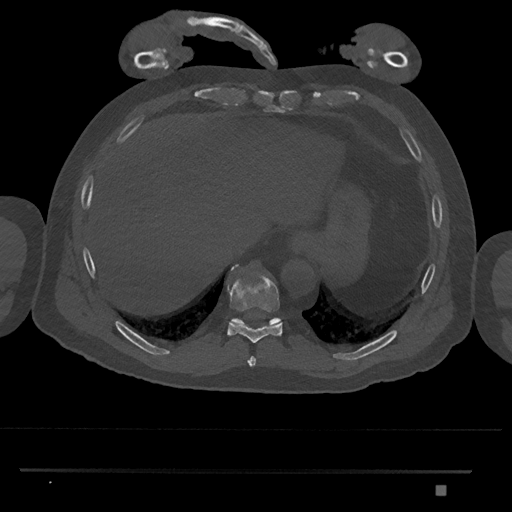
CT including the spine, one axial slice; position 1045 of 1134 along the scan axis; reconstruction kernel Br40s/3; bone window (W 1800 / L 400 HU); 0.5 mm slice thickness; 512 × 512 image matrix, field of view 429 × 429 mm. Male patient, age 65 years. Case-level facts recorded for this patient, not image findings: primary cancer: prostate.
Outlined on this slice (semi-automatically segmented with operator editing):
- T10 vertebra: bounding box (x1, y1, x2, y2) in pixels: (232, 318, 281, 325)
- T8 vertebra: (247, 356, 256, 366)
- T9 vertebra: (227, 265, 282, 343)